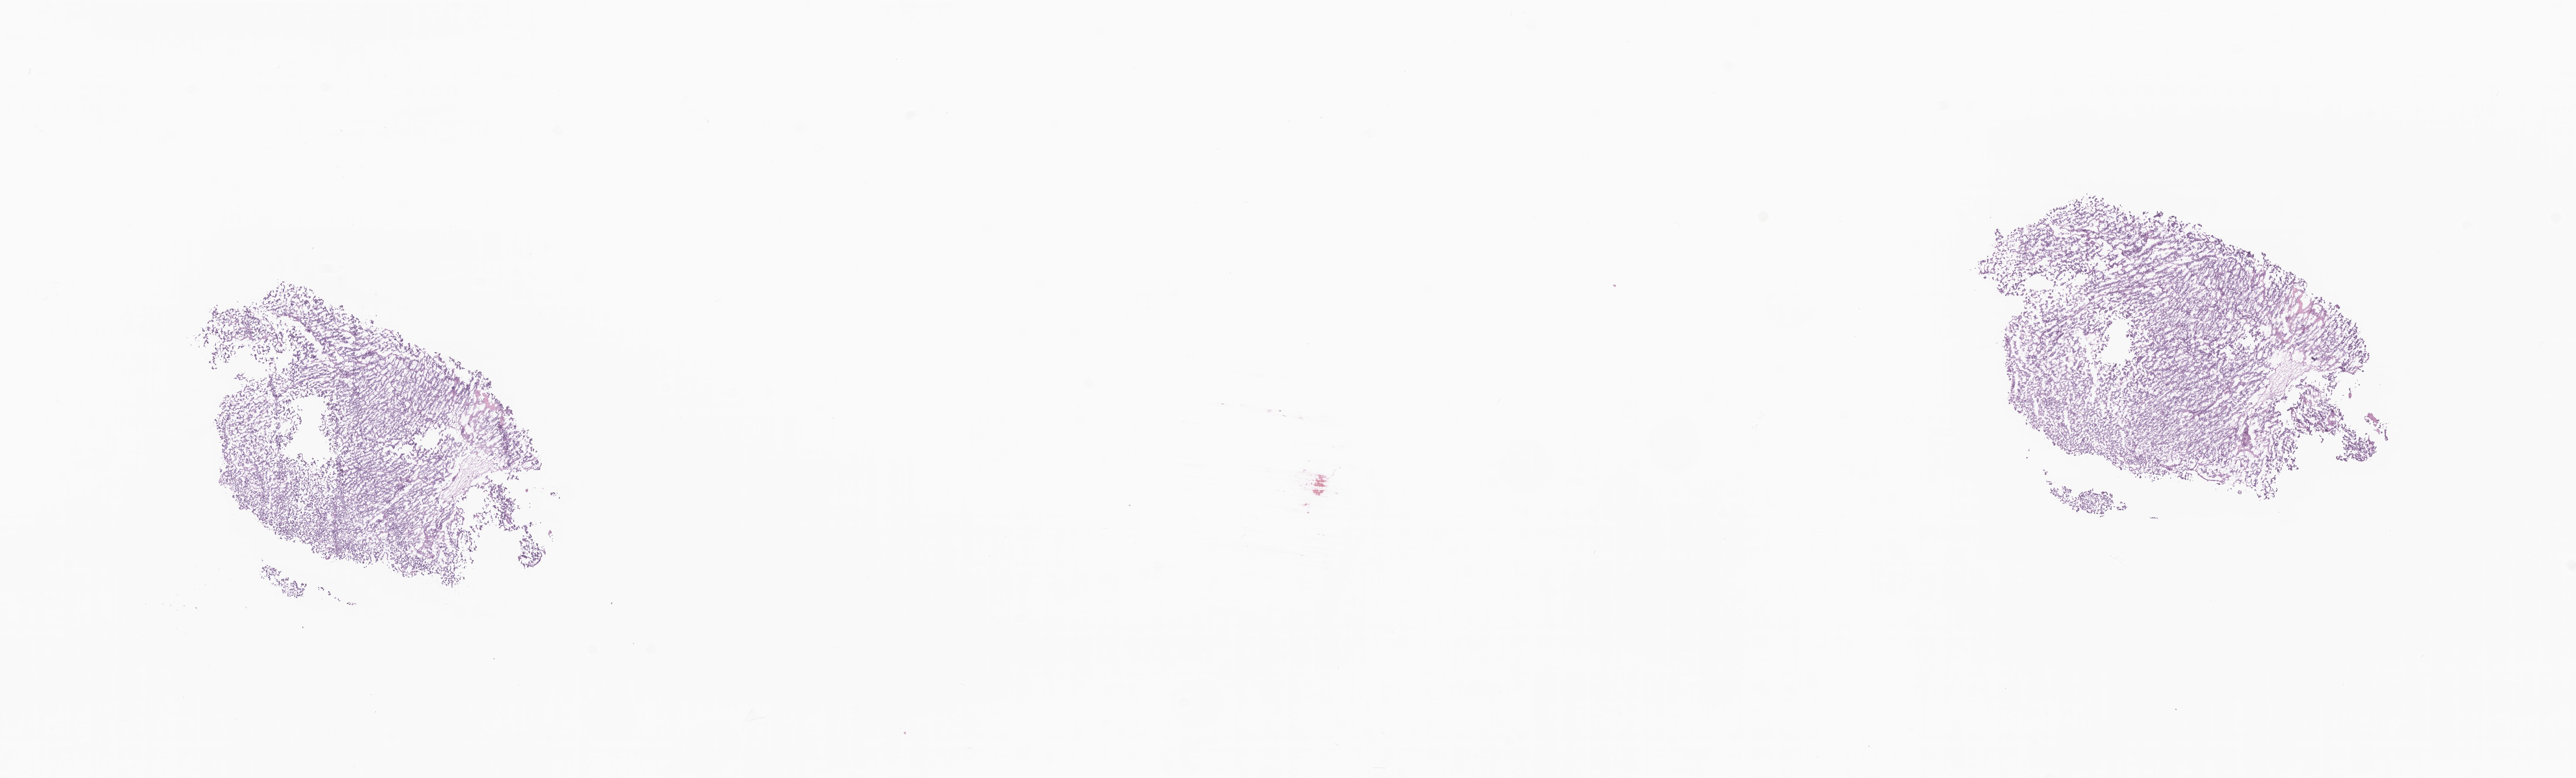
Whole-slide image, haematoxylin and eosin stain of tumor tissue from the brain — shown as a low-resolution overview of the whole scanned area (about 24.9 x 7.5 mm); frozen section (OCT-embedded). Male patient, age 41 months (3 years 5 months).
Recorded diagnosis: Choroid plexus carcinoma.